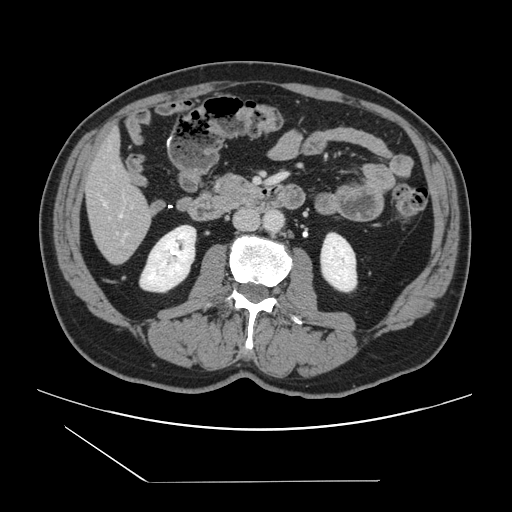
Contrast-enhanced abdominal CT, one axial slice; slice 38 of 157 in the series (ordered by position); intravenous contrast given; soft-tissue window (W 400 / L 40 HU); 512 × 512 image matrix. Male patient, age 61 years. Case-level facts recorded for this patient, not image findings: diagnosis: colorectal cancer liver metastases, imaged before liver resection; multiple liver metastases: yes; largest metastasis: 5.5 cm; disease in both lobes: yes.
Annotated regions visible in this slice (manually delineated by an expert):
- hepatic veins: box from (x=104, y=203) to (x=122, y=217) px
- liver: (x=85, y=133)–(x=153, y=263)
- planned liver remnant (the part of the liver to remain after resection): (x=85, y=133)–(x=148, y=219)
- portal vein (with intrahepatic branches): (x=125, y=232)–(x=128, y=234)